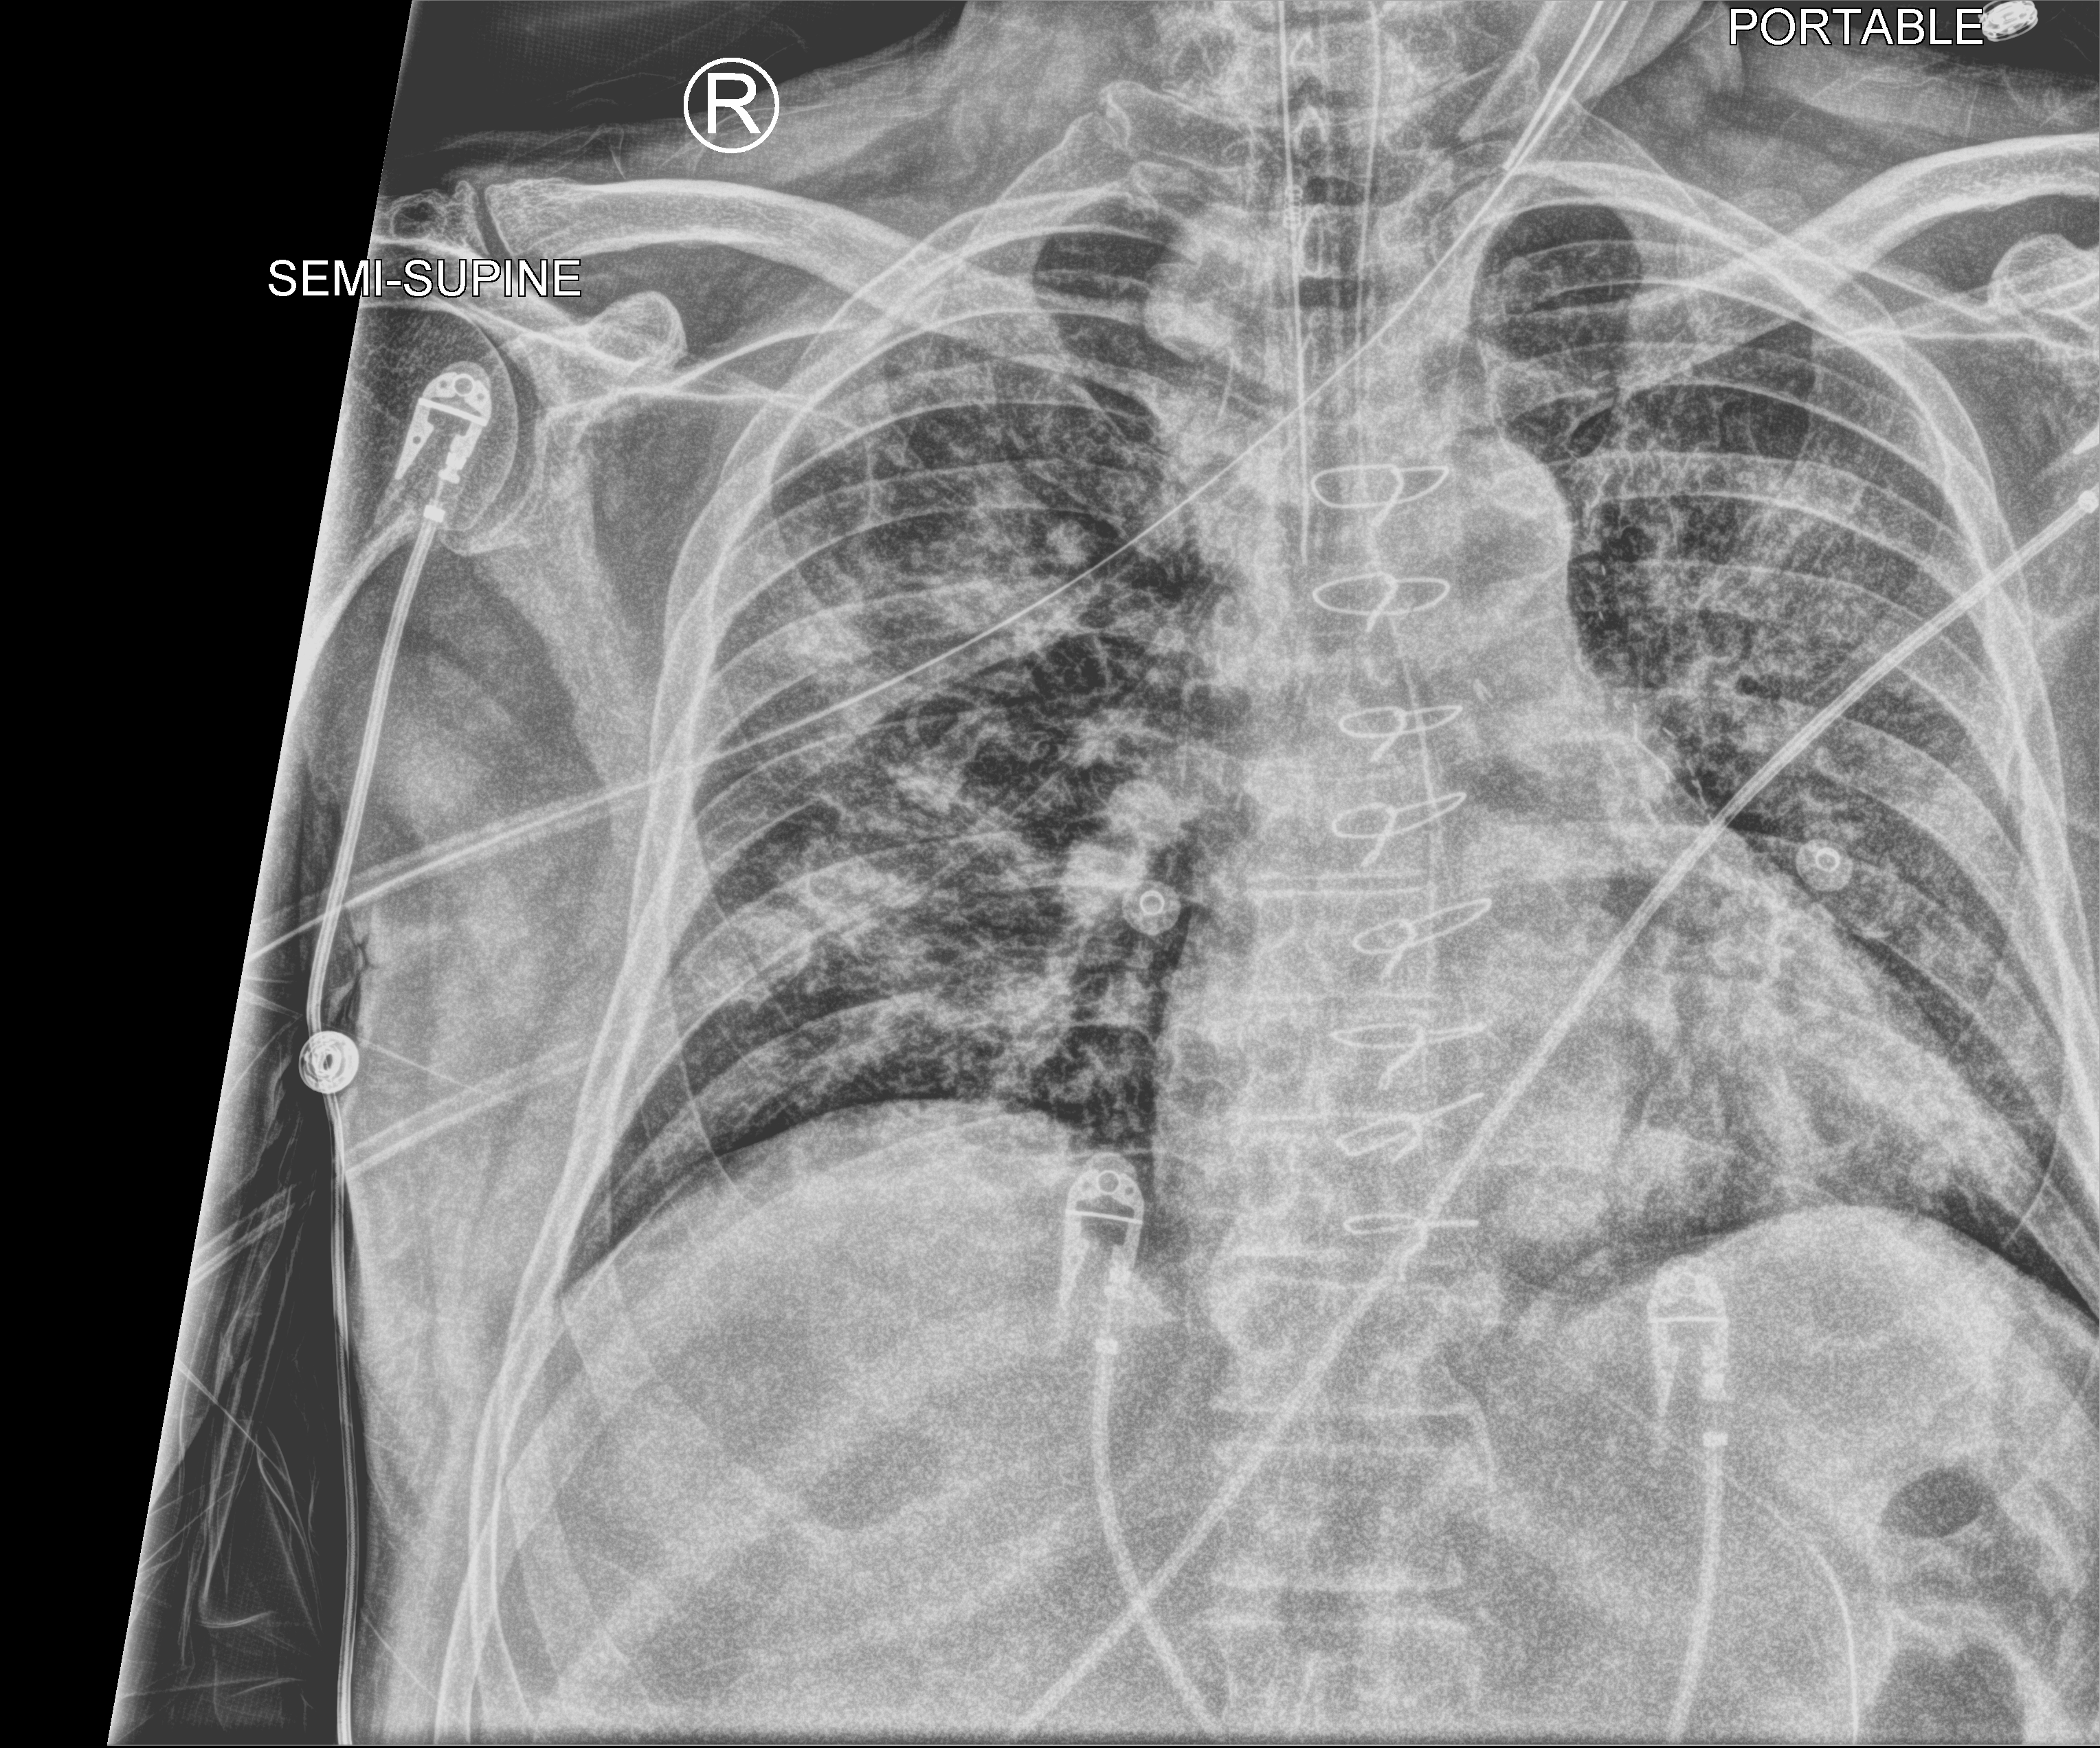
Chest X-ray (portable), anteroposterior (AP) projection. Male patient hospitalised with COVID-19, age 60–74 years.
Admission-level facts for this patient (not findings on this image; timing relative to this image not recorded):
- length of hospital stay: 22 days
- mechanically ventilated during this hospital stay: yes
- admitted to intensive care during this hospital stay: yes